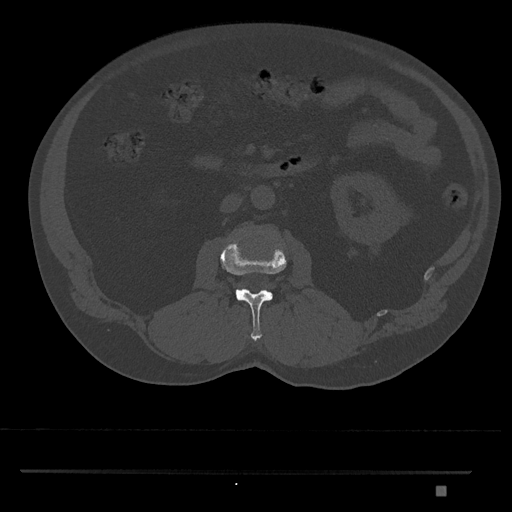
CT including the spine, one axial slice. Reconstruction kernel Br40s/3. Bone window (W 1800 / L 400 HU). 512 × 512 image matrix, field of view 429 × 429 mm. Male patient, age 65 years. From the clinical record (not read from this slice): primary cancer: prostate.
Structures marked on this image (semi-automatic segmentation, software-assisted and operator-edited):
- L2 vertebra: bounding box [x1, y1, x2, y2] px = [220, 240, 287, 341]